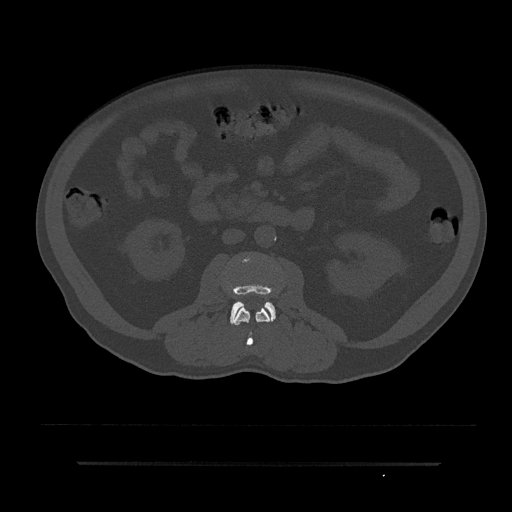
CT including the spine, one axial slice. Position 37 of 797 along the scan axis. Reconstruction kernel Br40s/3. 120 kVp. Bone window (W 1800 / L 400 HU). 0.5 mm slice thickness. 512 × 512 image matrix, field of view 464 × 464 mm. Patient: male, 59 years. Case-level facts recorded for this patient, not image findings: primary cancer: bile ducts; vertebrae with lytic lesions (as recorded): T10.
Outlined on this slice (semi-automatic segmentation, software-assisted and operator-edited):
- L2 vertebra: bounding box <233,306,272,346> (left, top, right, bottom; pixels)
- L3 vertebra: <230,285,276,324>